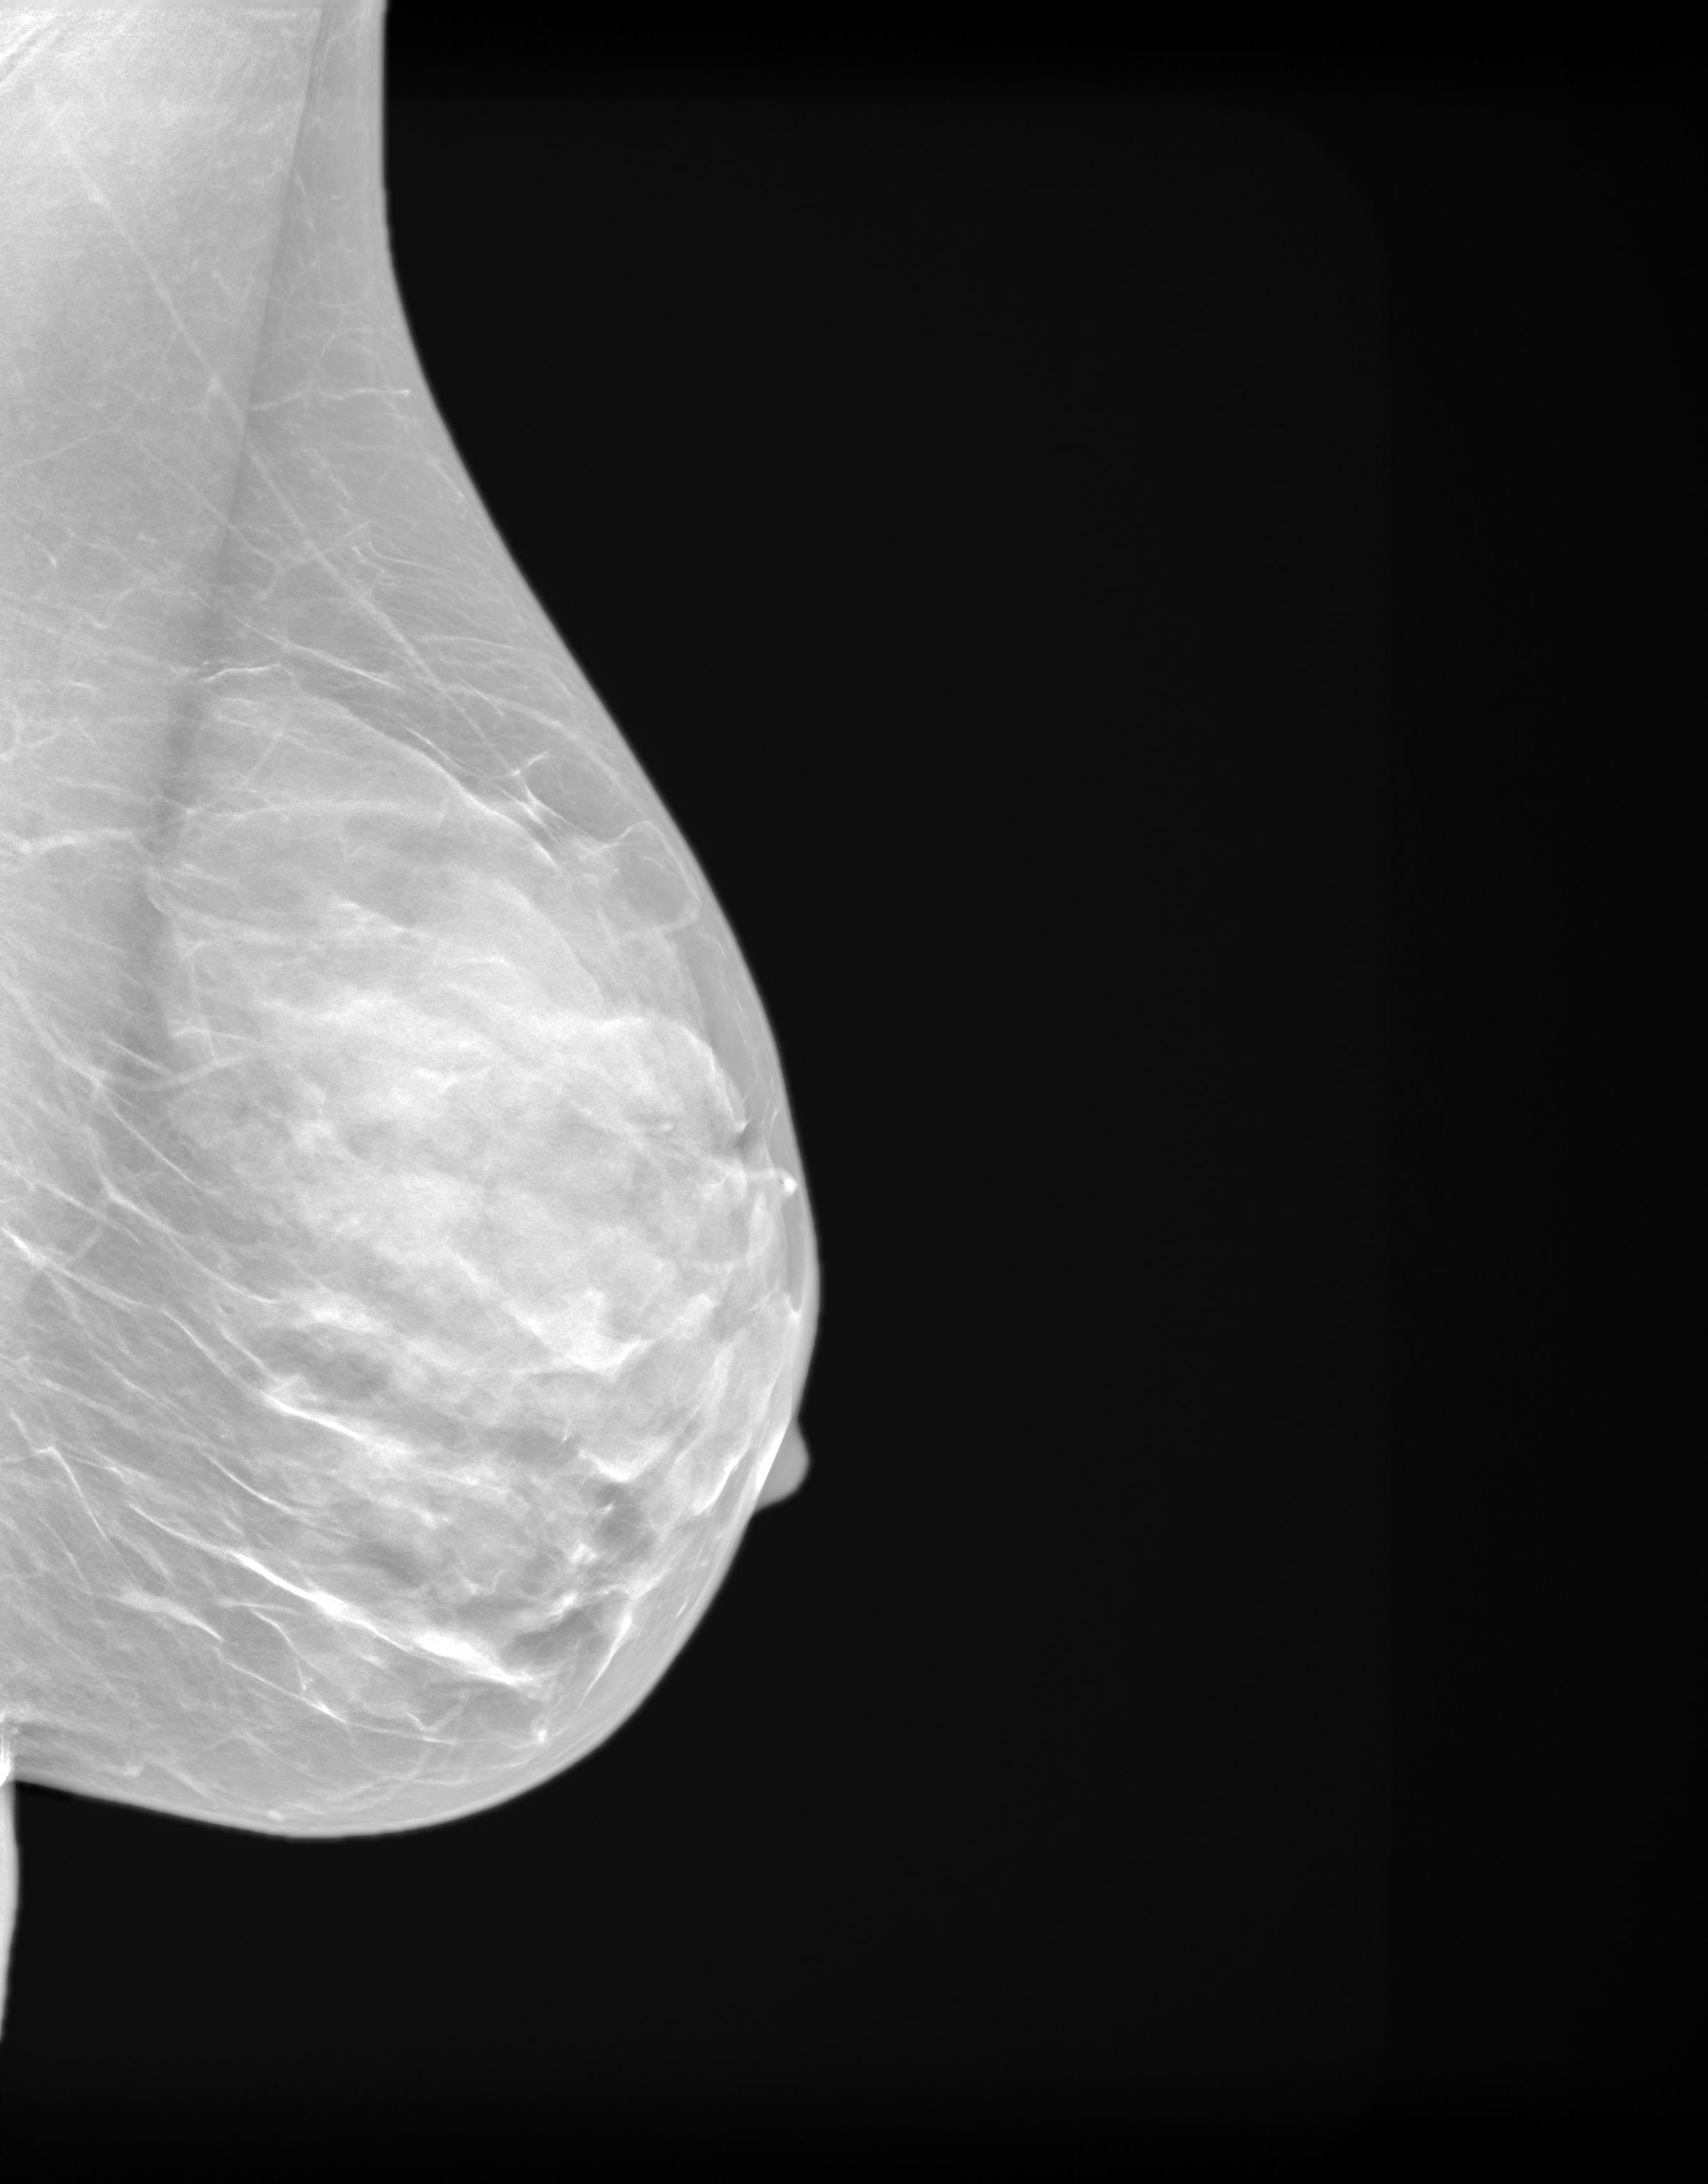
Annual screening mammography examination. Patient aged 60 years (female).
Image type: synthesized 2-D view from tomosynthesis. Breast: left. Projection: mediolateral oblique (MLO) view.